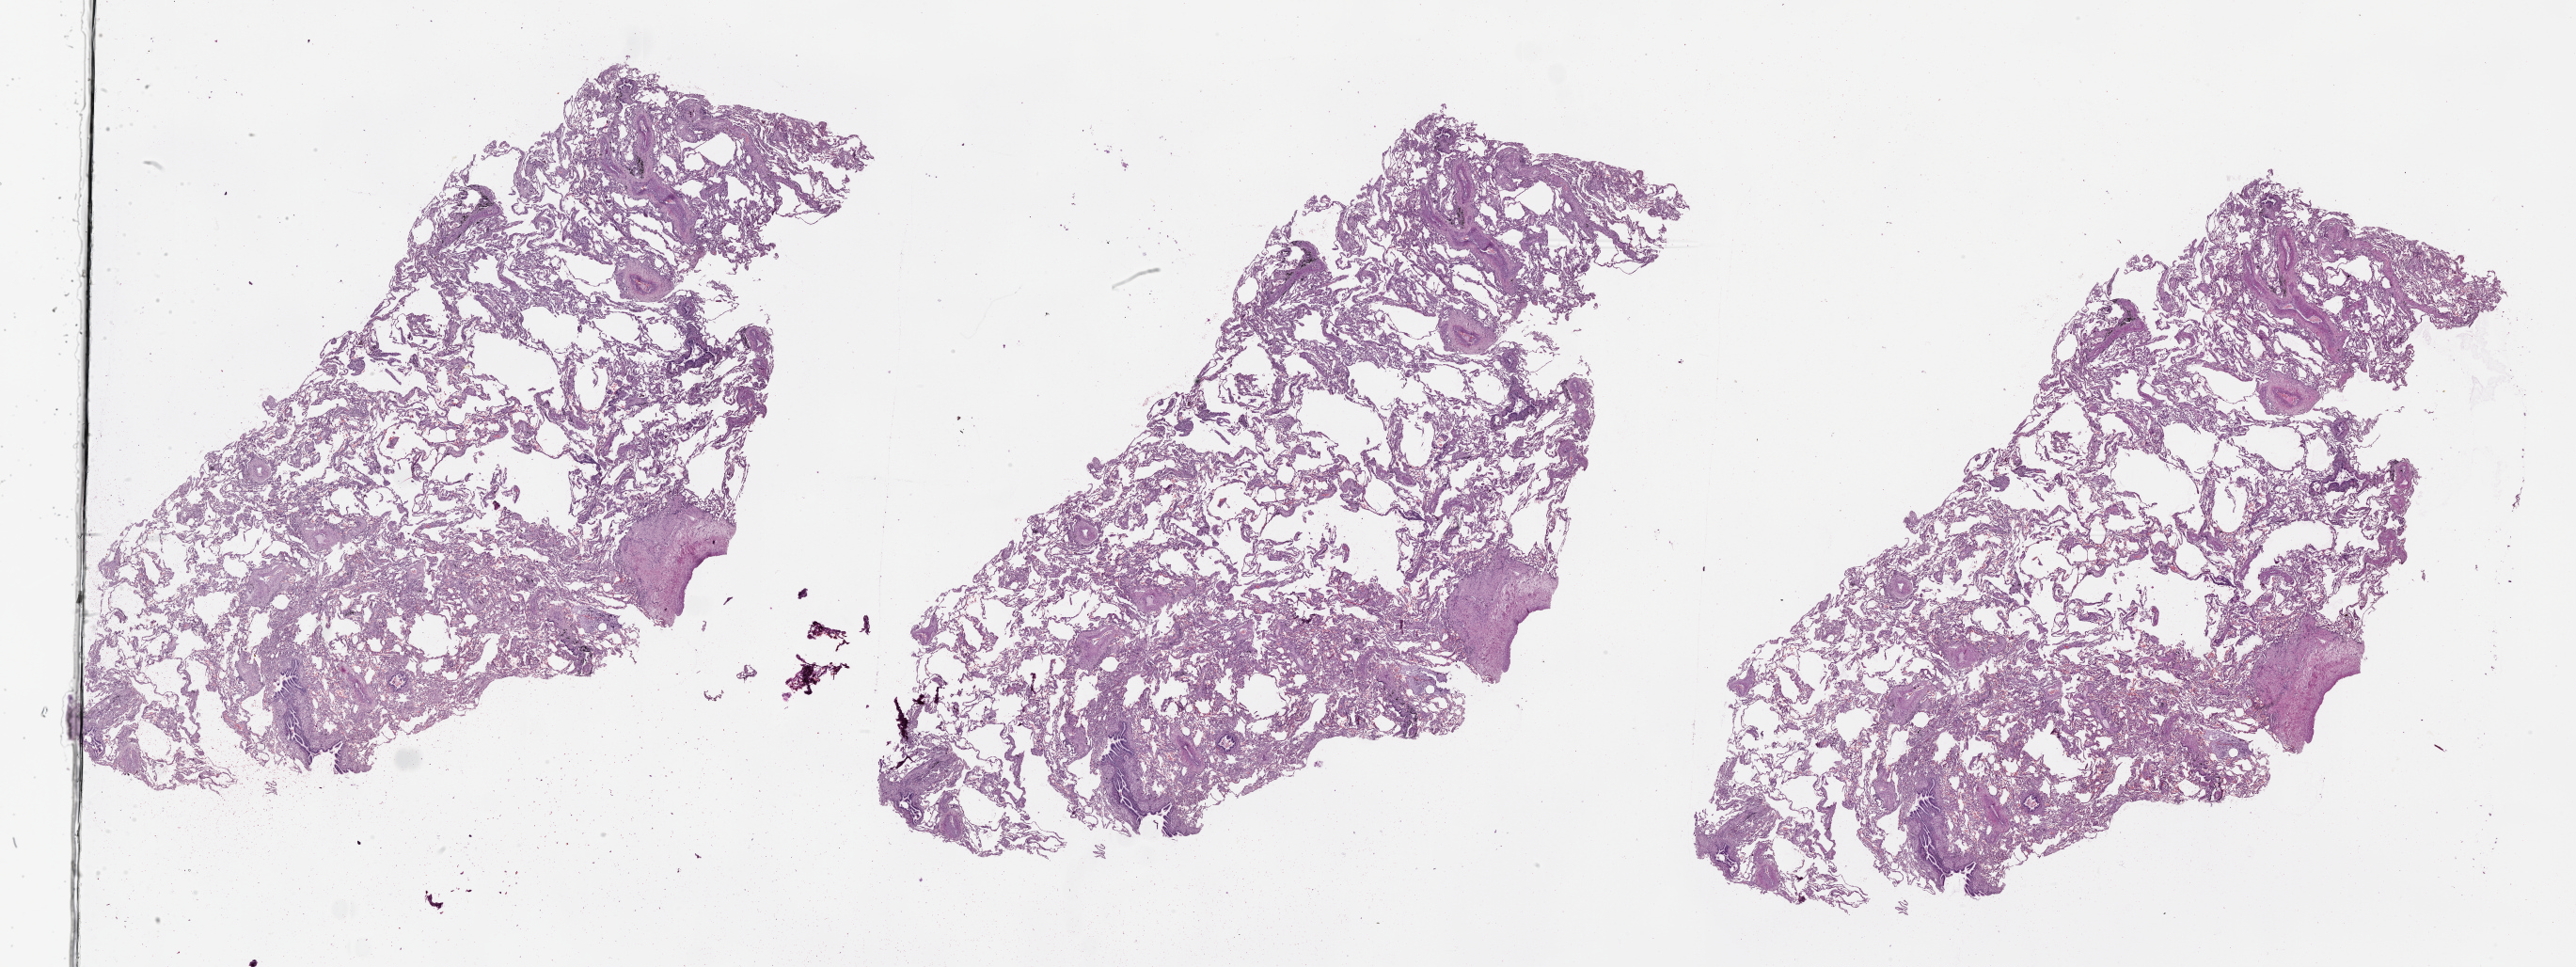
Whole-slide histology image, Hematoxylin and eosin (H&E) stained — low-resolution overview of the scanned area, about 44.1 x 16.5 mm. Normal (non-tumour) tissue sample, lung. 72-year-old male patient.
This section: normal (non-tumour) tissue from the same patient. Patient diagnosis (cohort enrolment): squamous cell carcinoma (lung).